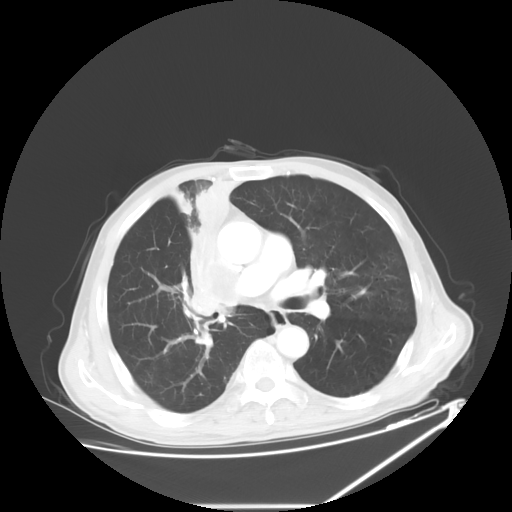
Chest CT, one axial slice. Slice 36 of 60 in the series (ordered by position). Reconstruction kernel STANDARD. Lung window (W 1500 / L -600 HU). 5 mm slice thickness. 512 × 512 image matrix, field of view 410 × 410 mm. Patient: male, 73 years. From the clinical record (not read from this slice): clinical TNM (as recorded): T2a N1 M0.
Annotated regions visible in this slice (rectangle marked by the reading radiologist):
- lung tumour (recorded histology: squamous cell carcinoma): bounding box (x1, y1, x2, y2) in pixels: (175, 166, 251, 321)